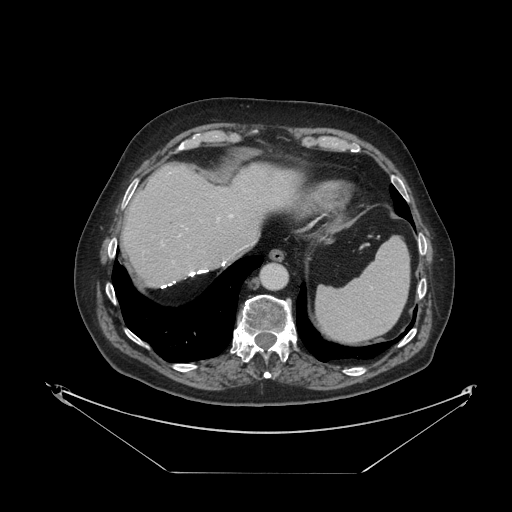
Contrast-enhanced abdominal CT, one axial slice. Position 97 of 121 along the scan axis. Reconstruction kernel STANDARD. 120 kVp. Intravenous contrast given. Soft-tissue window (W 400 / L 40 HU). 2.5 mm slice thickness. 512 × 512 image matrix, field of view 500 × 500 mm. Male patient, age 68 years. Case-level facts recorded for this patient, not image findings: diagnosis: colorectal cancer liver metastases, imaged before liver resection; multiple liver metastases: no; largest metastasis: 4 cm; chemotherapy before resection: yes.
Annotated regions visible in this slice (expert manual segmentation):
- hepatic veins: box from (x=179, y=215) to (x=233, y=236) px
- liver: (x=123, y=163)–(x=296, y=286)
- planned liver remnant (the part of the liver to remain after resection): (x=123, y=163)–(x=296, y=286)
- portal vein (with intrahepatic branches): (x=162, y=218)–(x=219, y=263)